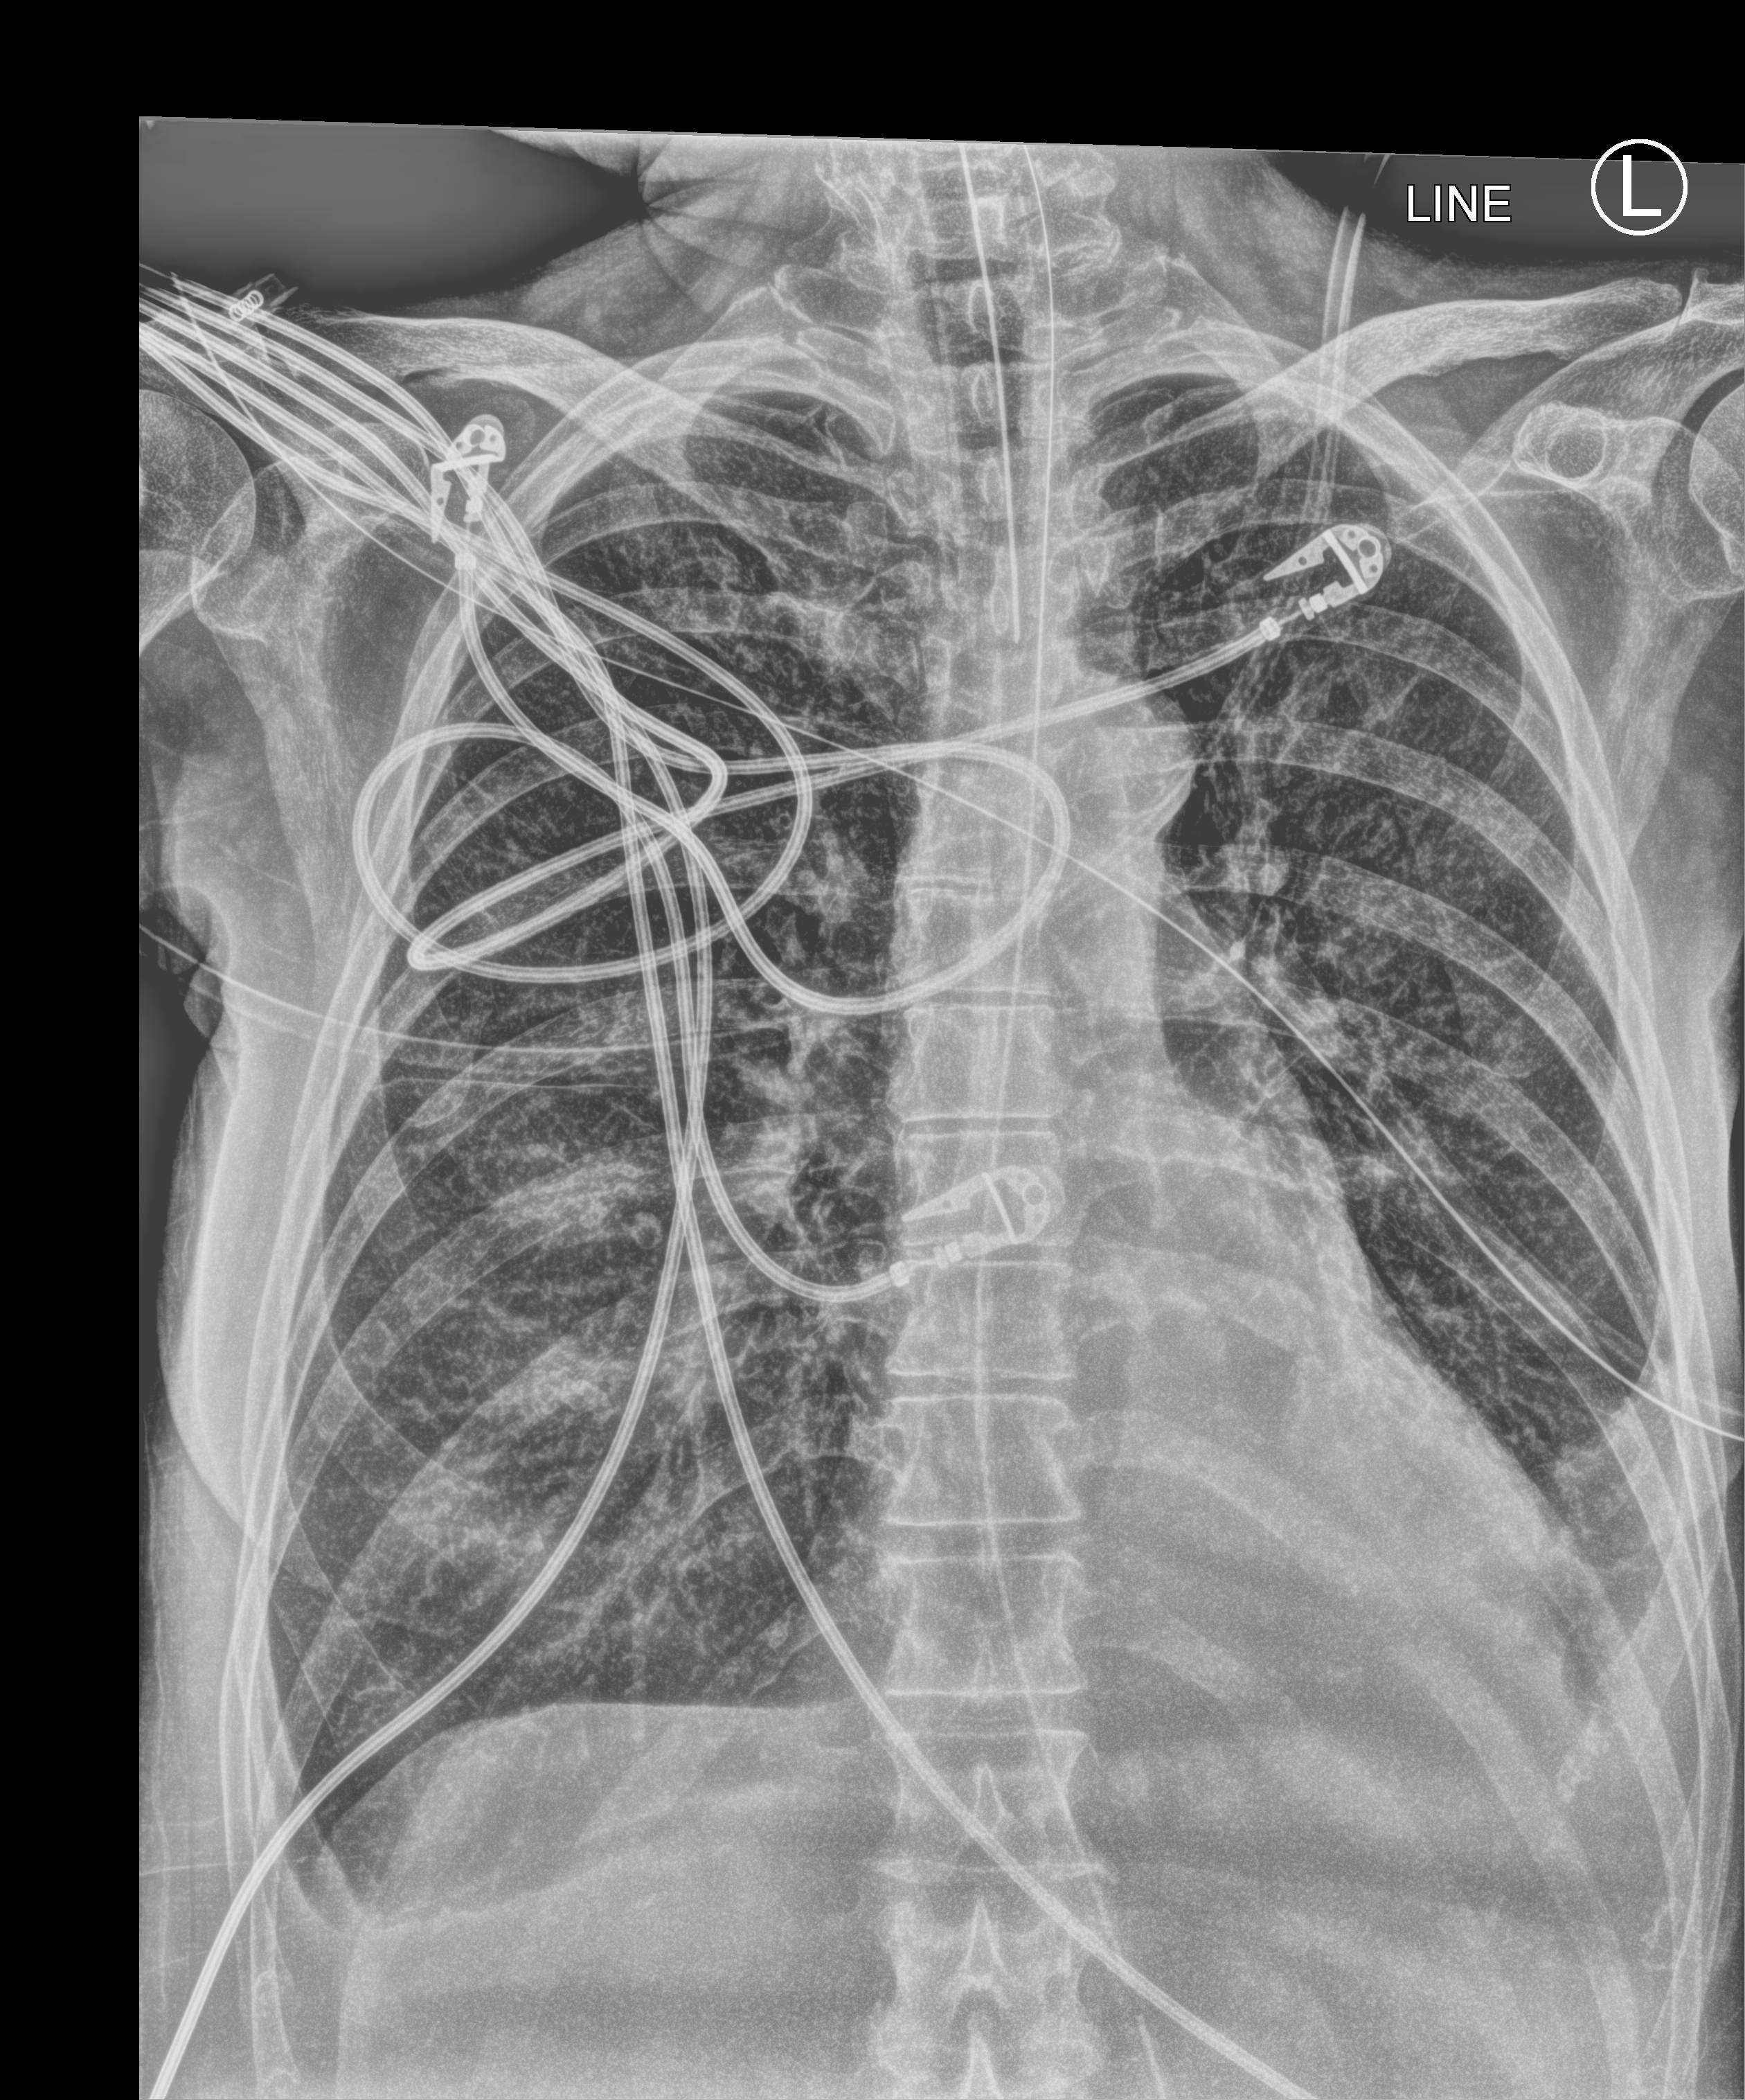
Portable chest radiograph. Patient hospitalised with COVID-19; female, aged 60–74 years.
Admission-level facts for this patient (not findings on this image; timing relative to this image not recorded): mechanically ventilated during this hospital stay: yes.